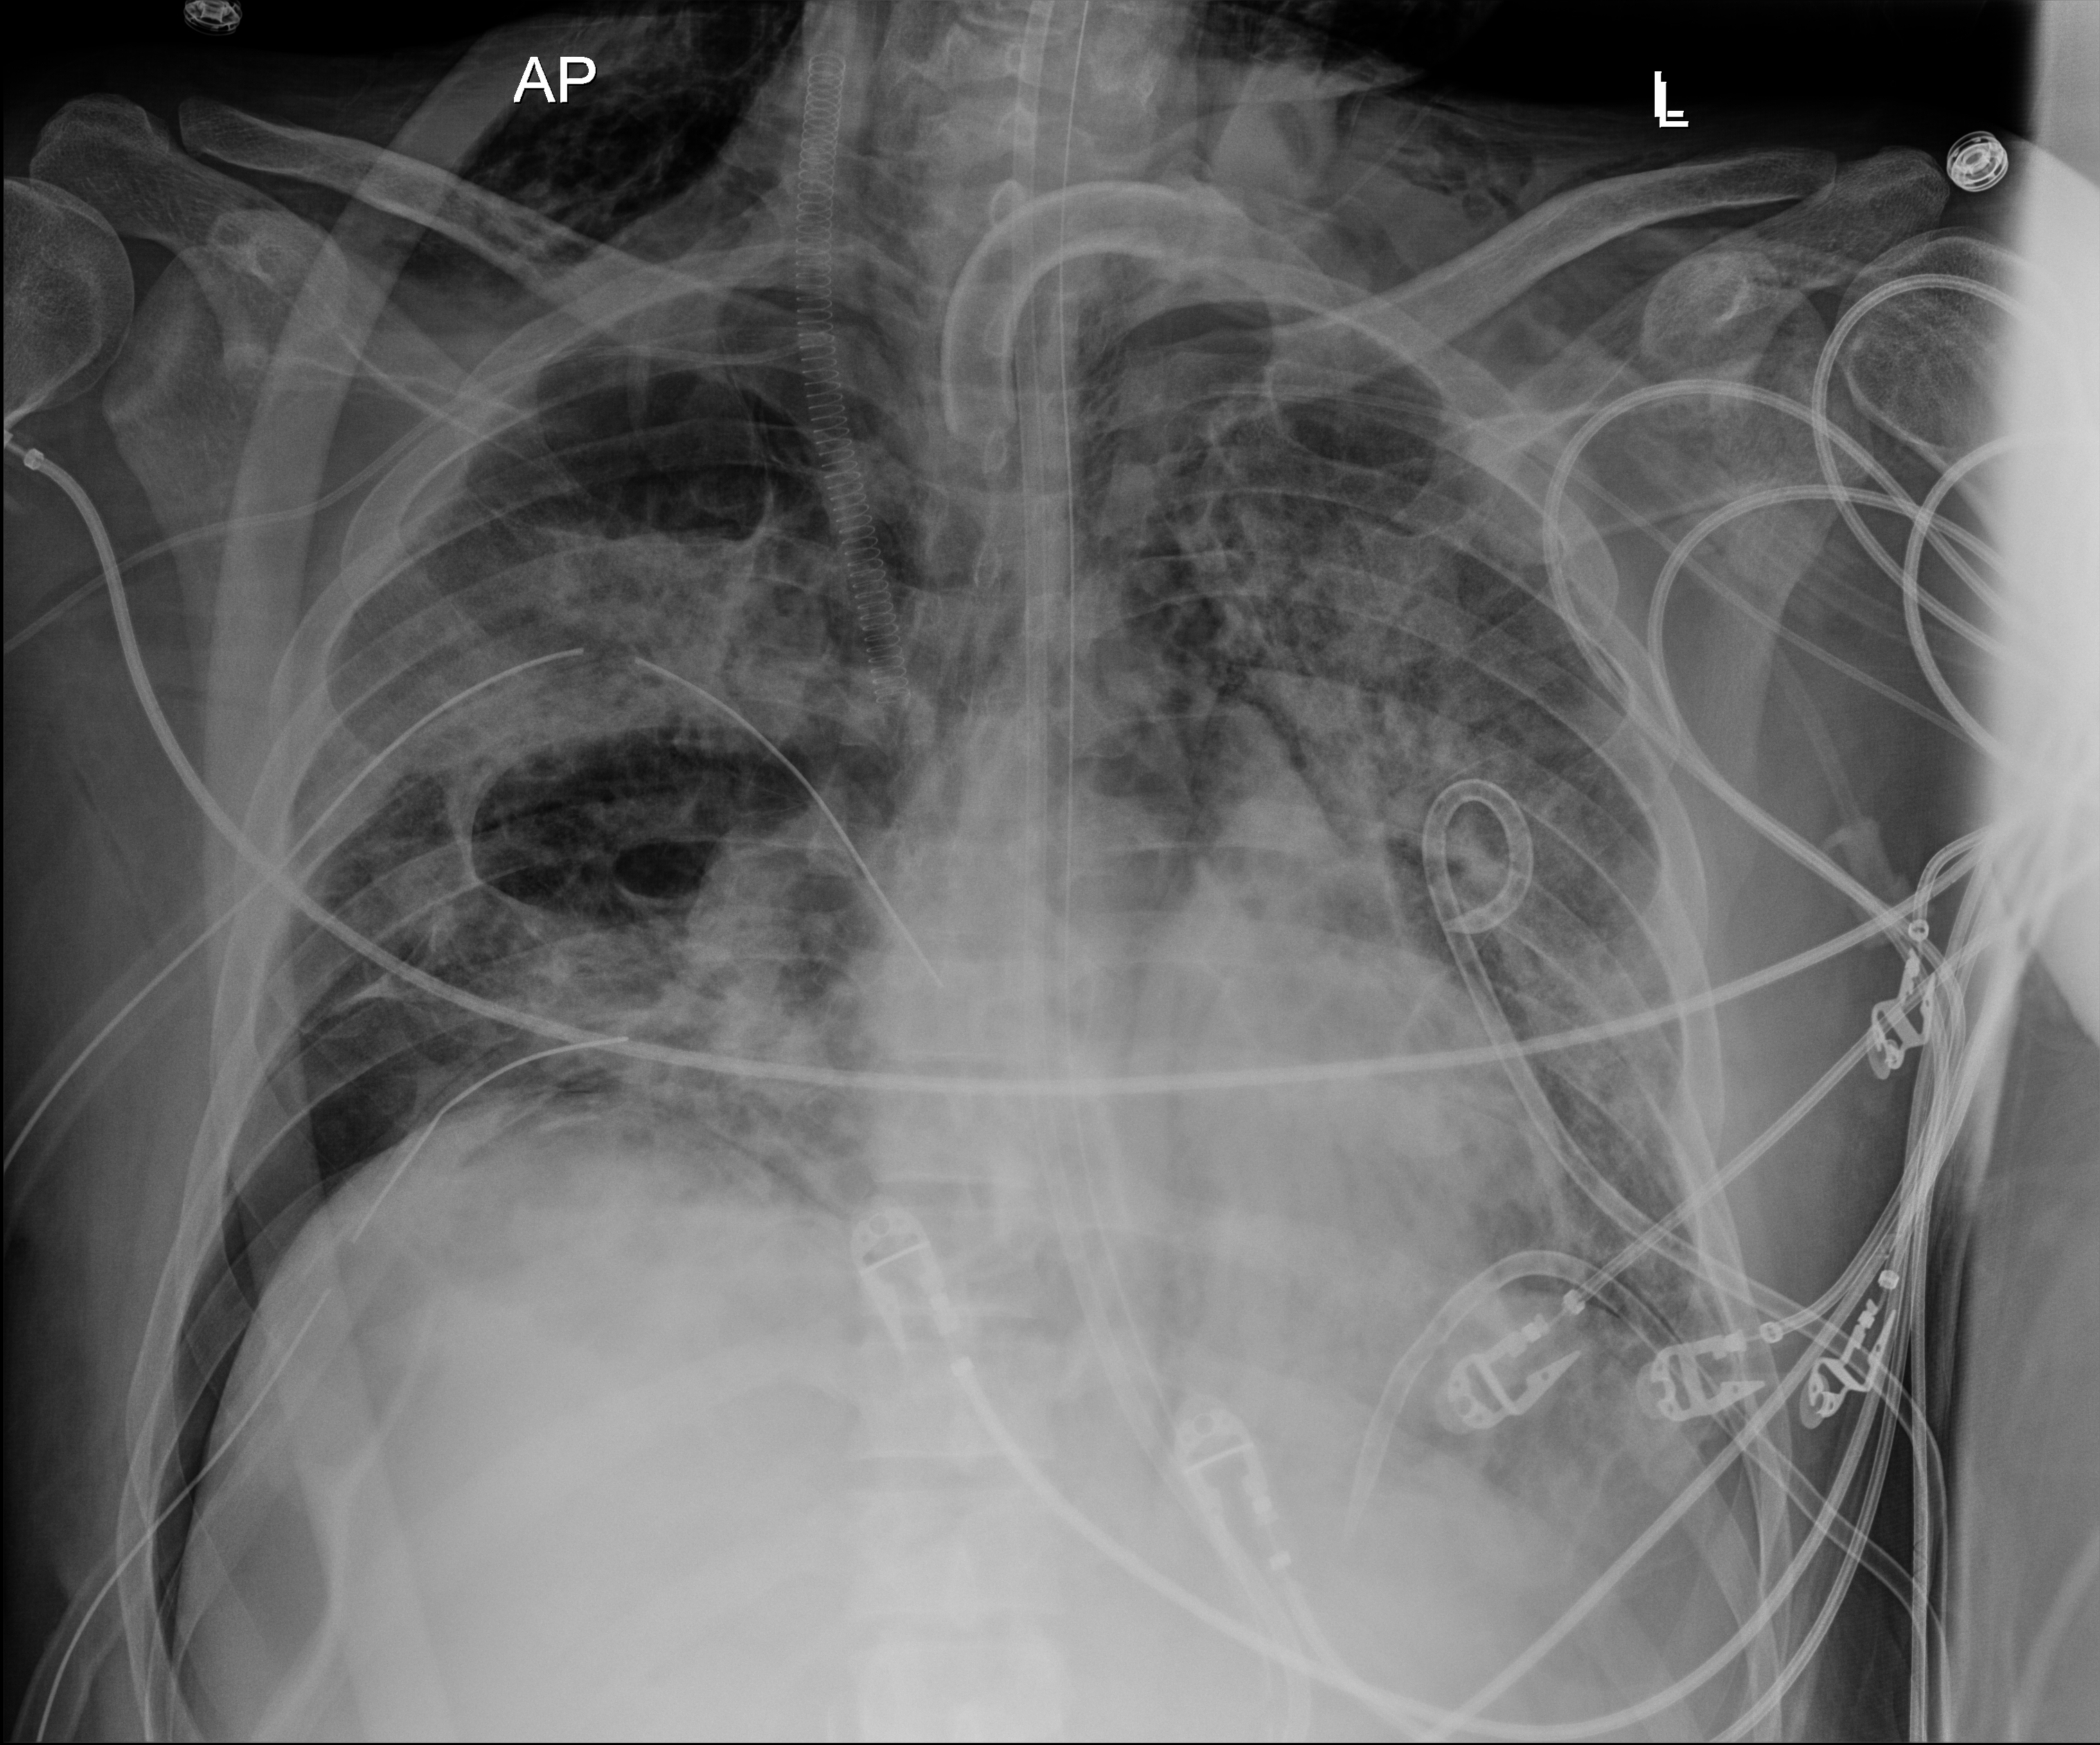
Chest X-ray (portable), anteroposterior (AP) projection. Patient hospitalised with COVID-19, aged 18–59 years.
Admission-level facts for this patient (not findings on this image; timing relative to this image not recorded): chronic kidney disease (admission record): no; other chronic lung disease (admission record): no; admitted to intensive care during this hospital stay: yes.